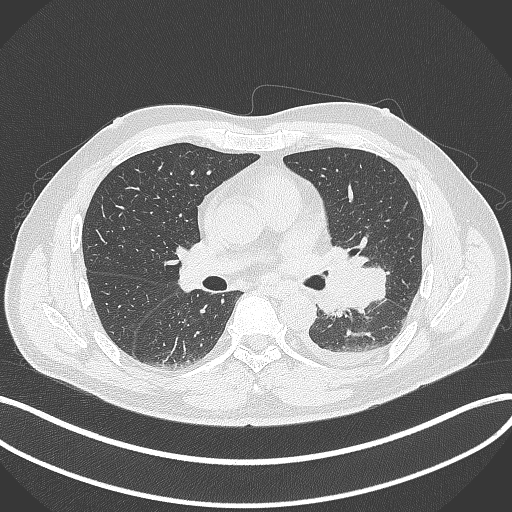
Chest CT, one axial slice; slice 195 of 342 in the series (ordered by position); reconstruction kernel B70f; 120 kVp; lung window (W 1500 / L -600 HU); 1 mm slice thickness; 512 × 512 image matrix, field of view 400 × 400 mm. Patient: male, 58 years. Case-level facts recorded for this patient, not image findings: clinical TNM (as recorded): T3 N1 M1b.
Annotated regions visible in this slice (bounding box drawn by a radiologist):
- lung tumour (recorded histology: small cell carcinoma): bounding box <314,255,393,323> (left, top, right, bottom; pixels)